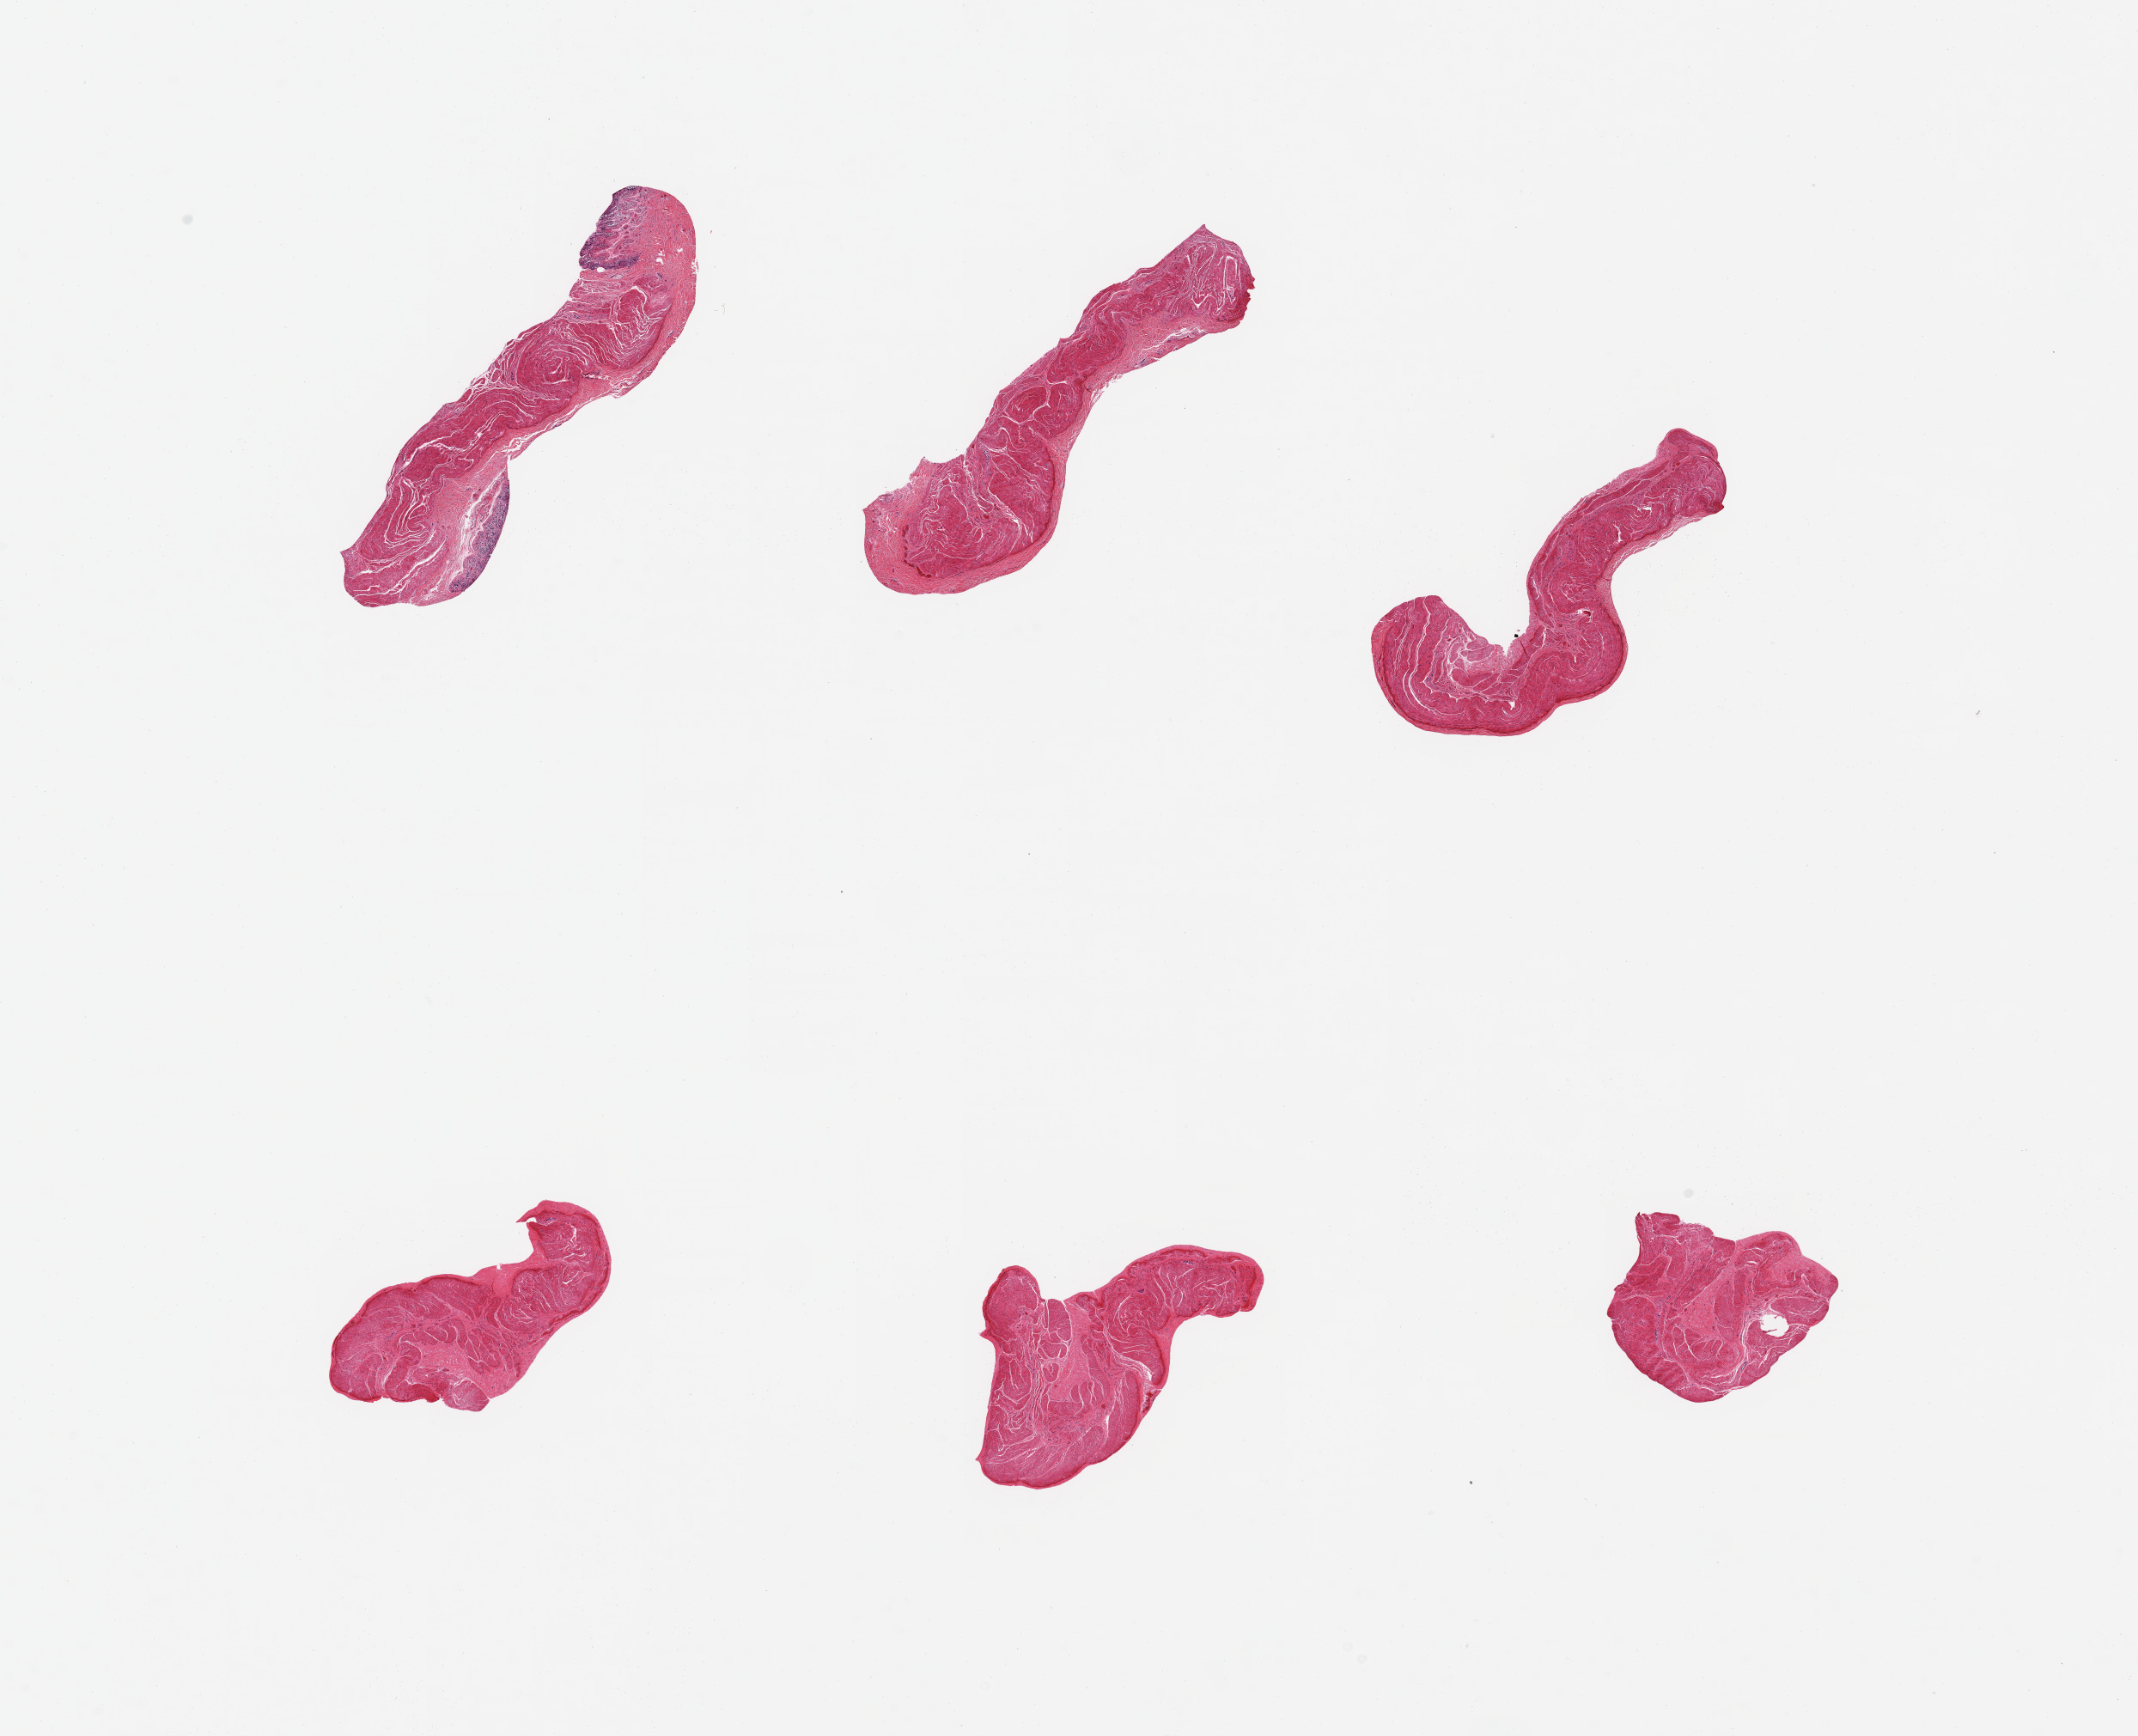
Digitized H&E-stained section — whole scanned area (about 19.7 x 16.0 mm) shown as a low-resolution overview, PAXgene-fixed, paraffin-embedded tissue, sampled site (target tissue): sigmoid colon, tissue donor sample. Male donor.
Reviewer comment on this tissue sample: 6 pieces, confirmed target muscularis.